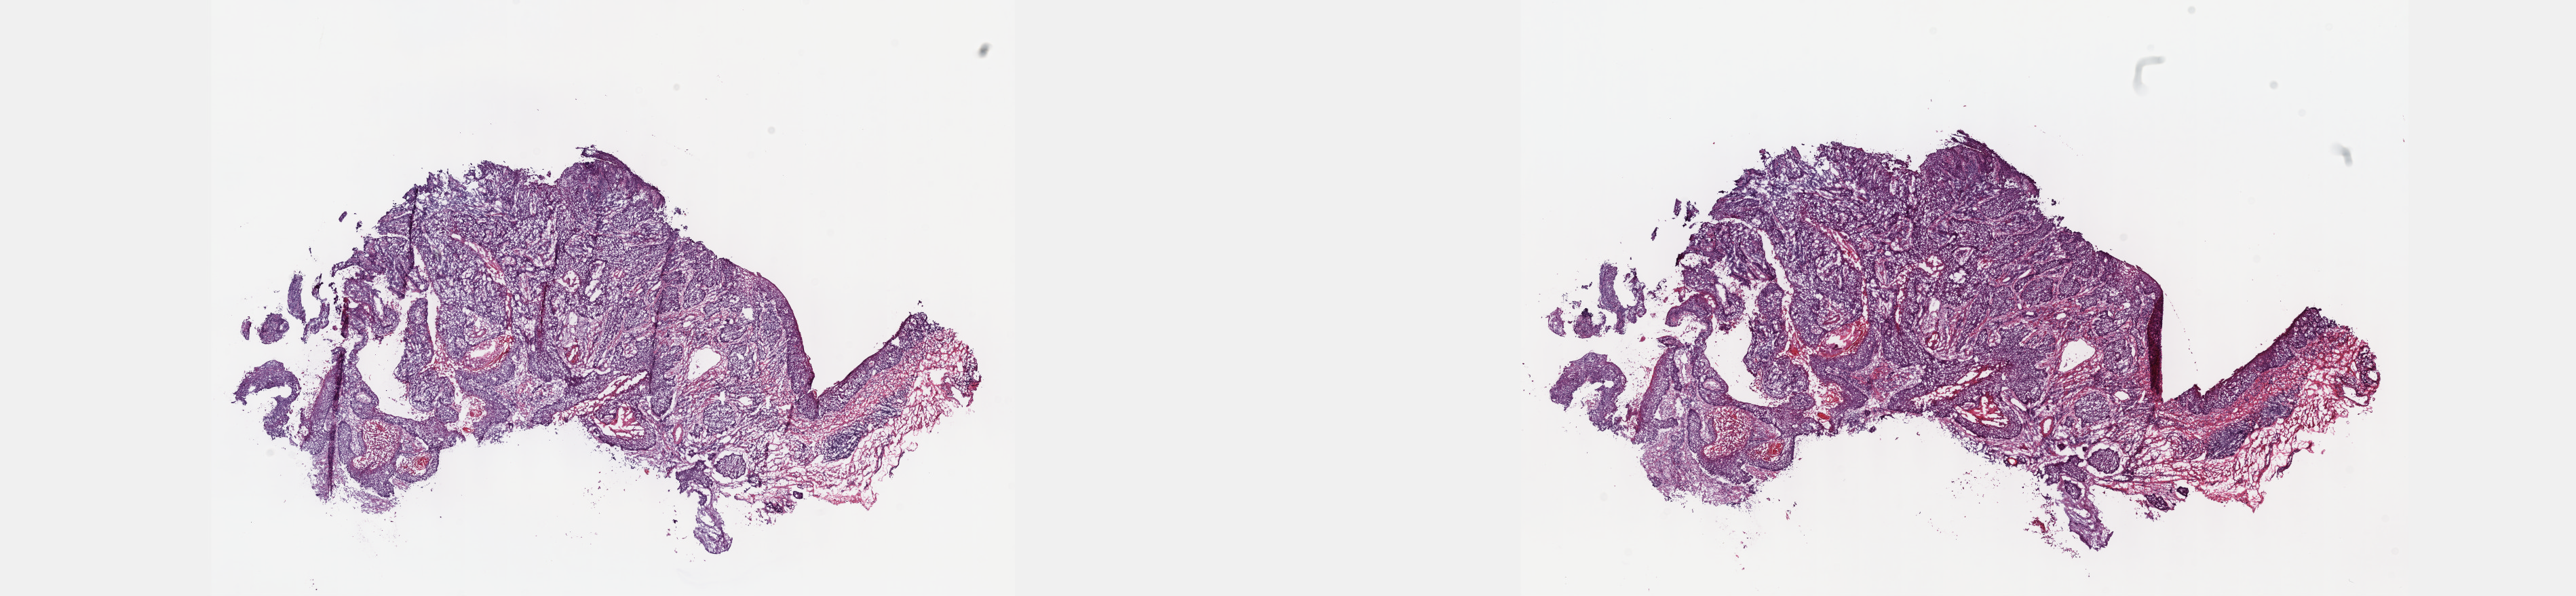
H&E whole-slide image — low-resolution overview of the scanned area, about 30.7 x 7.1 mm (acquisition: 40x scan); frozen section; sample: primary tumour, esophagus. Male patient; age at initial diagnosis 53 years. Histologic grade: G2 (moderately differentiated). Pathologist review of this section (percent, as recorded): tumour cells 60%, tumour nuclei 70%, normal cells 10%, stromal cells 30%, necrosis 0%. Inflammatory infiltration, as recorded: lymphocyte infiltration 0%, monocyte infiltration 0%, neutrophil infiltration 0%.
* AJCC pathologic stage: IIIA (7th edition)
* pathologic diagnosis: Squamous cell carcinoma, NOS (lower third of esophagus)